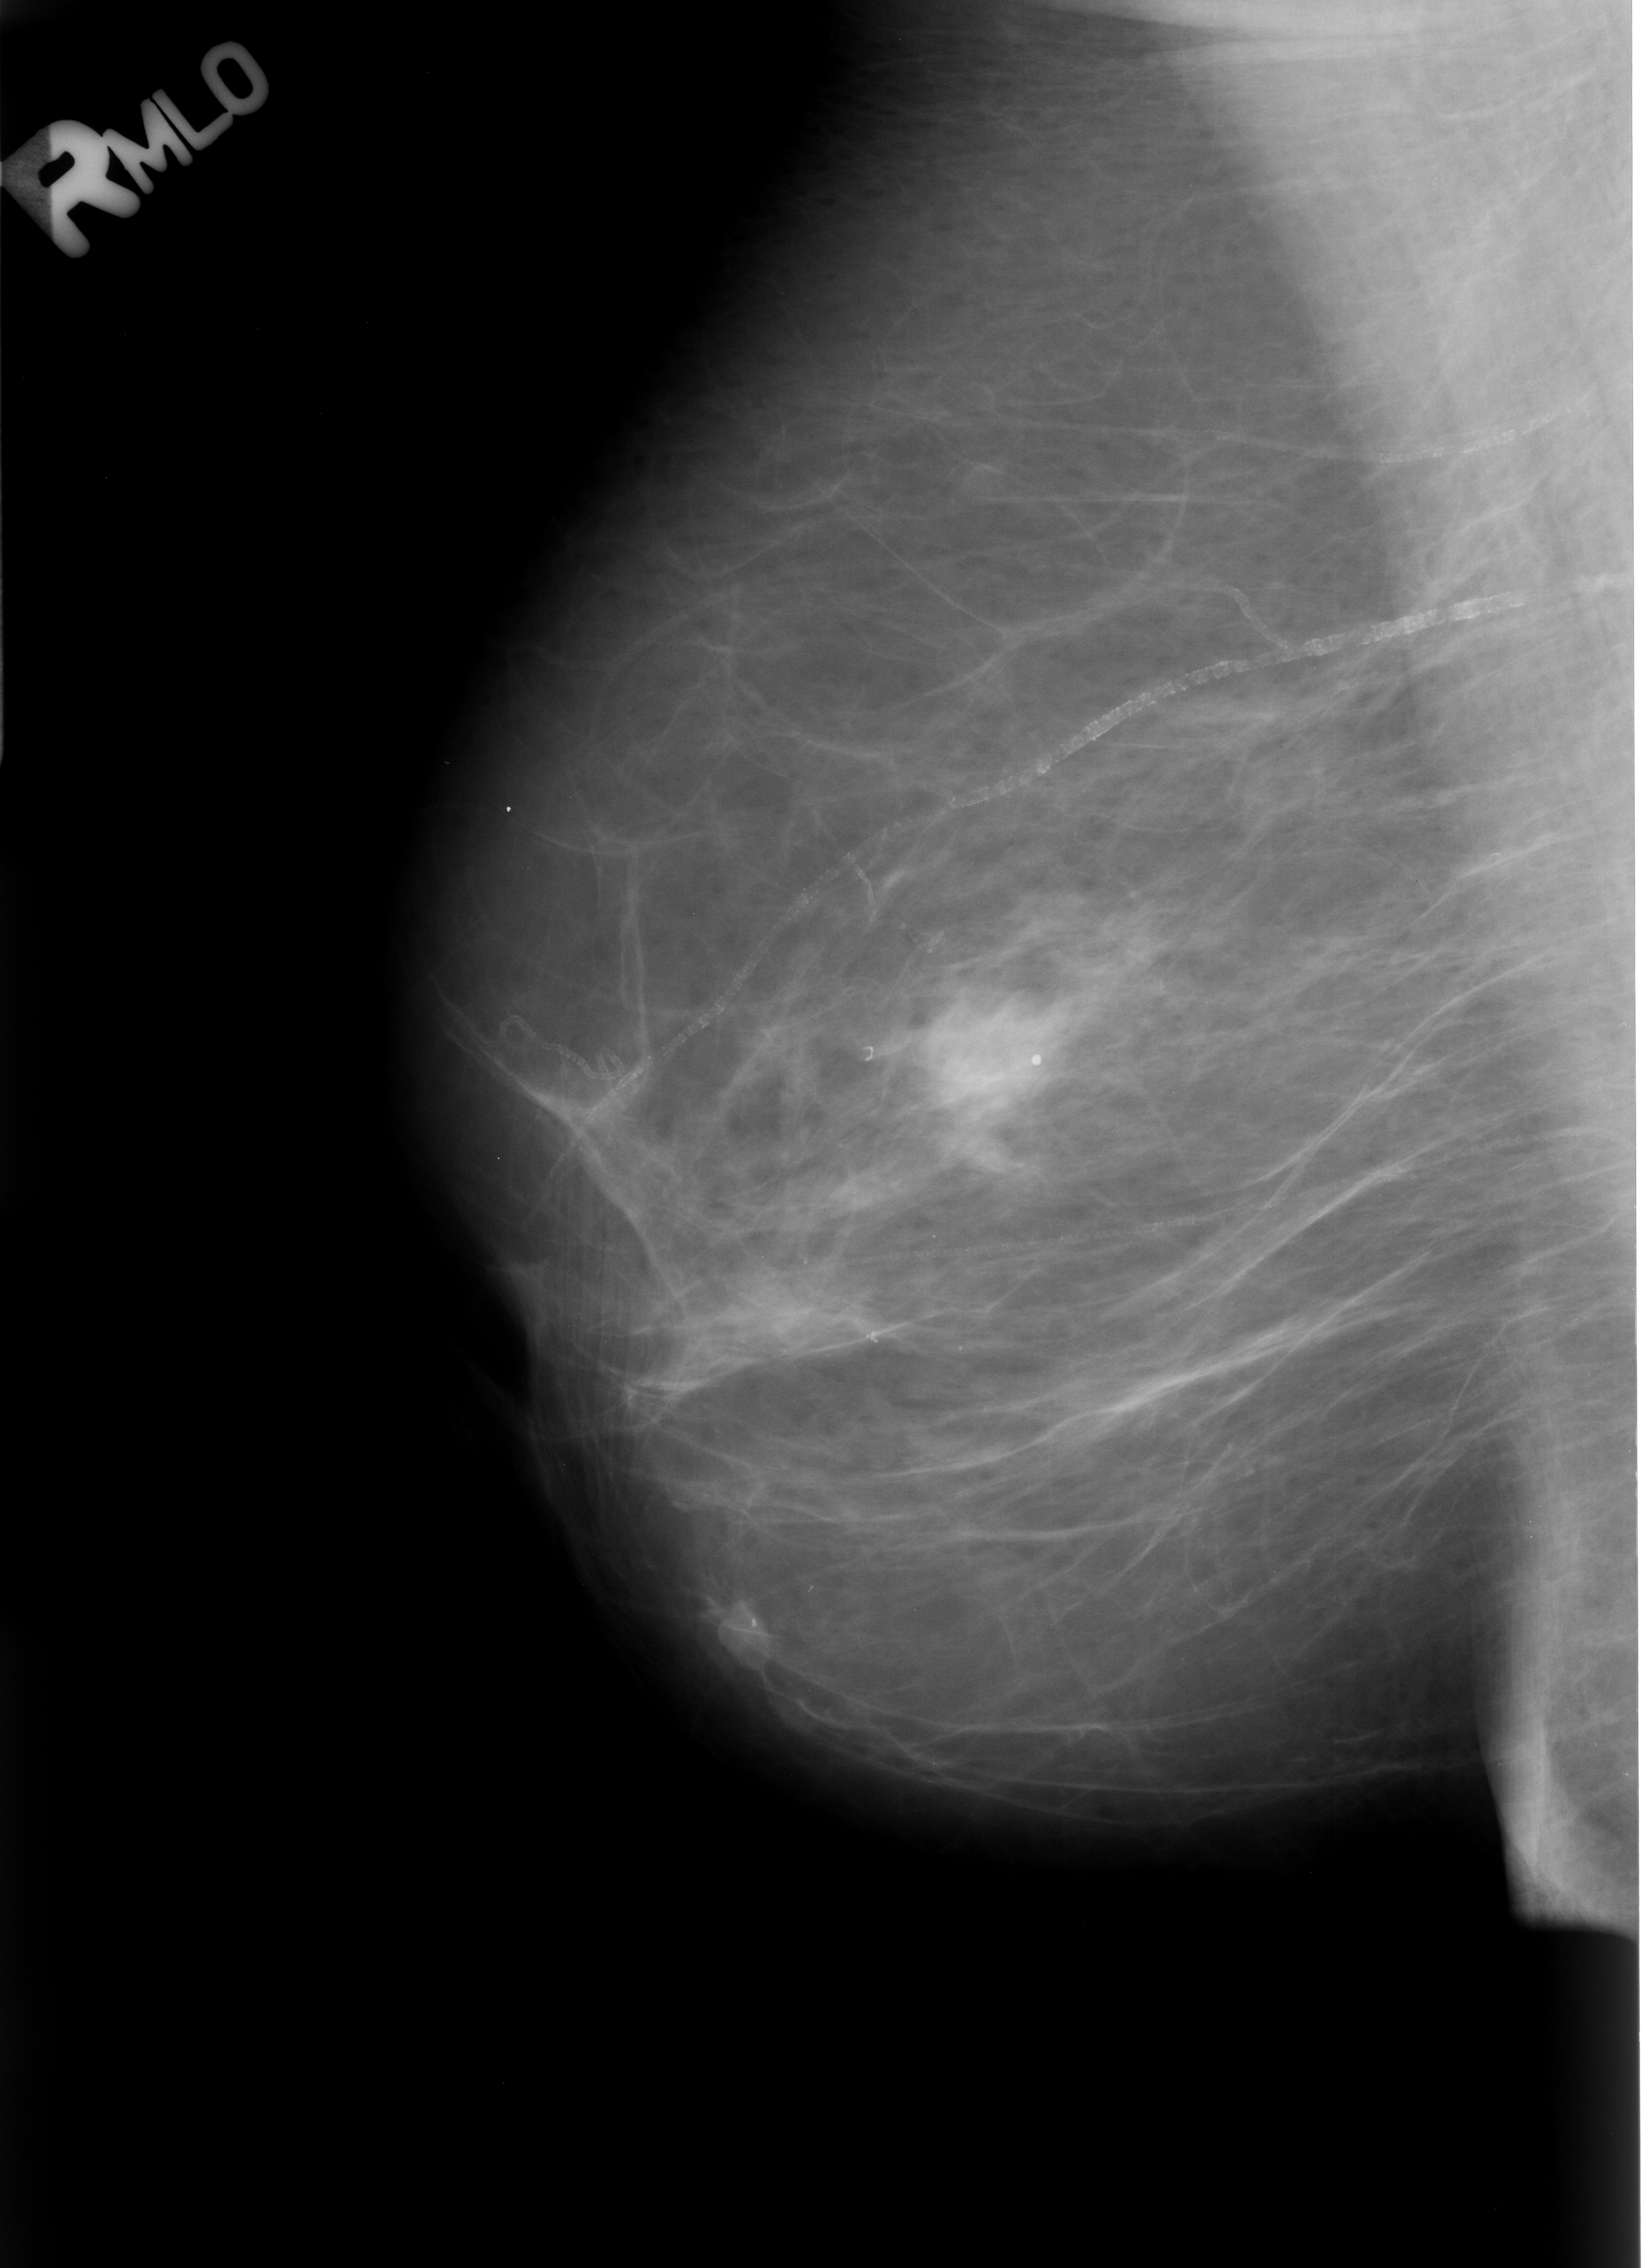
Mammogram (digitized film), right breast, MLO view, breast composition: scattered fibroglandular densities (BI-RADS density category 2 of 4).
Abnormality record for this image: Finding 1 of 2: calcifications, morphology round and regular; BI-RADS assessment category 2; subtlety rating 5 on a 1 (subtle) to 5 (obvious) scale; benign; no additional work-up was recommended (benign without callback). Finding 2 of 2: calcifications, morphology vascular; BI-RADS assessment category 2; subtlety rating 5 on a 1 (subtle) to 5 (obvious) scale; benign; no additional work-up was recommended (benign without callback).